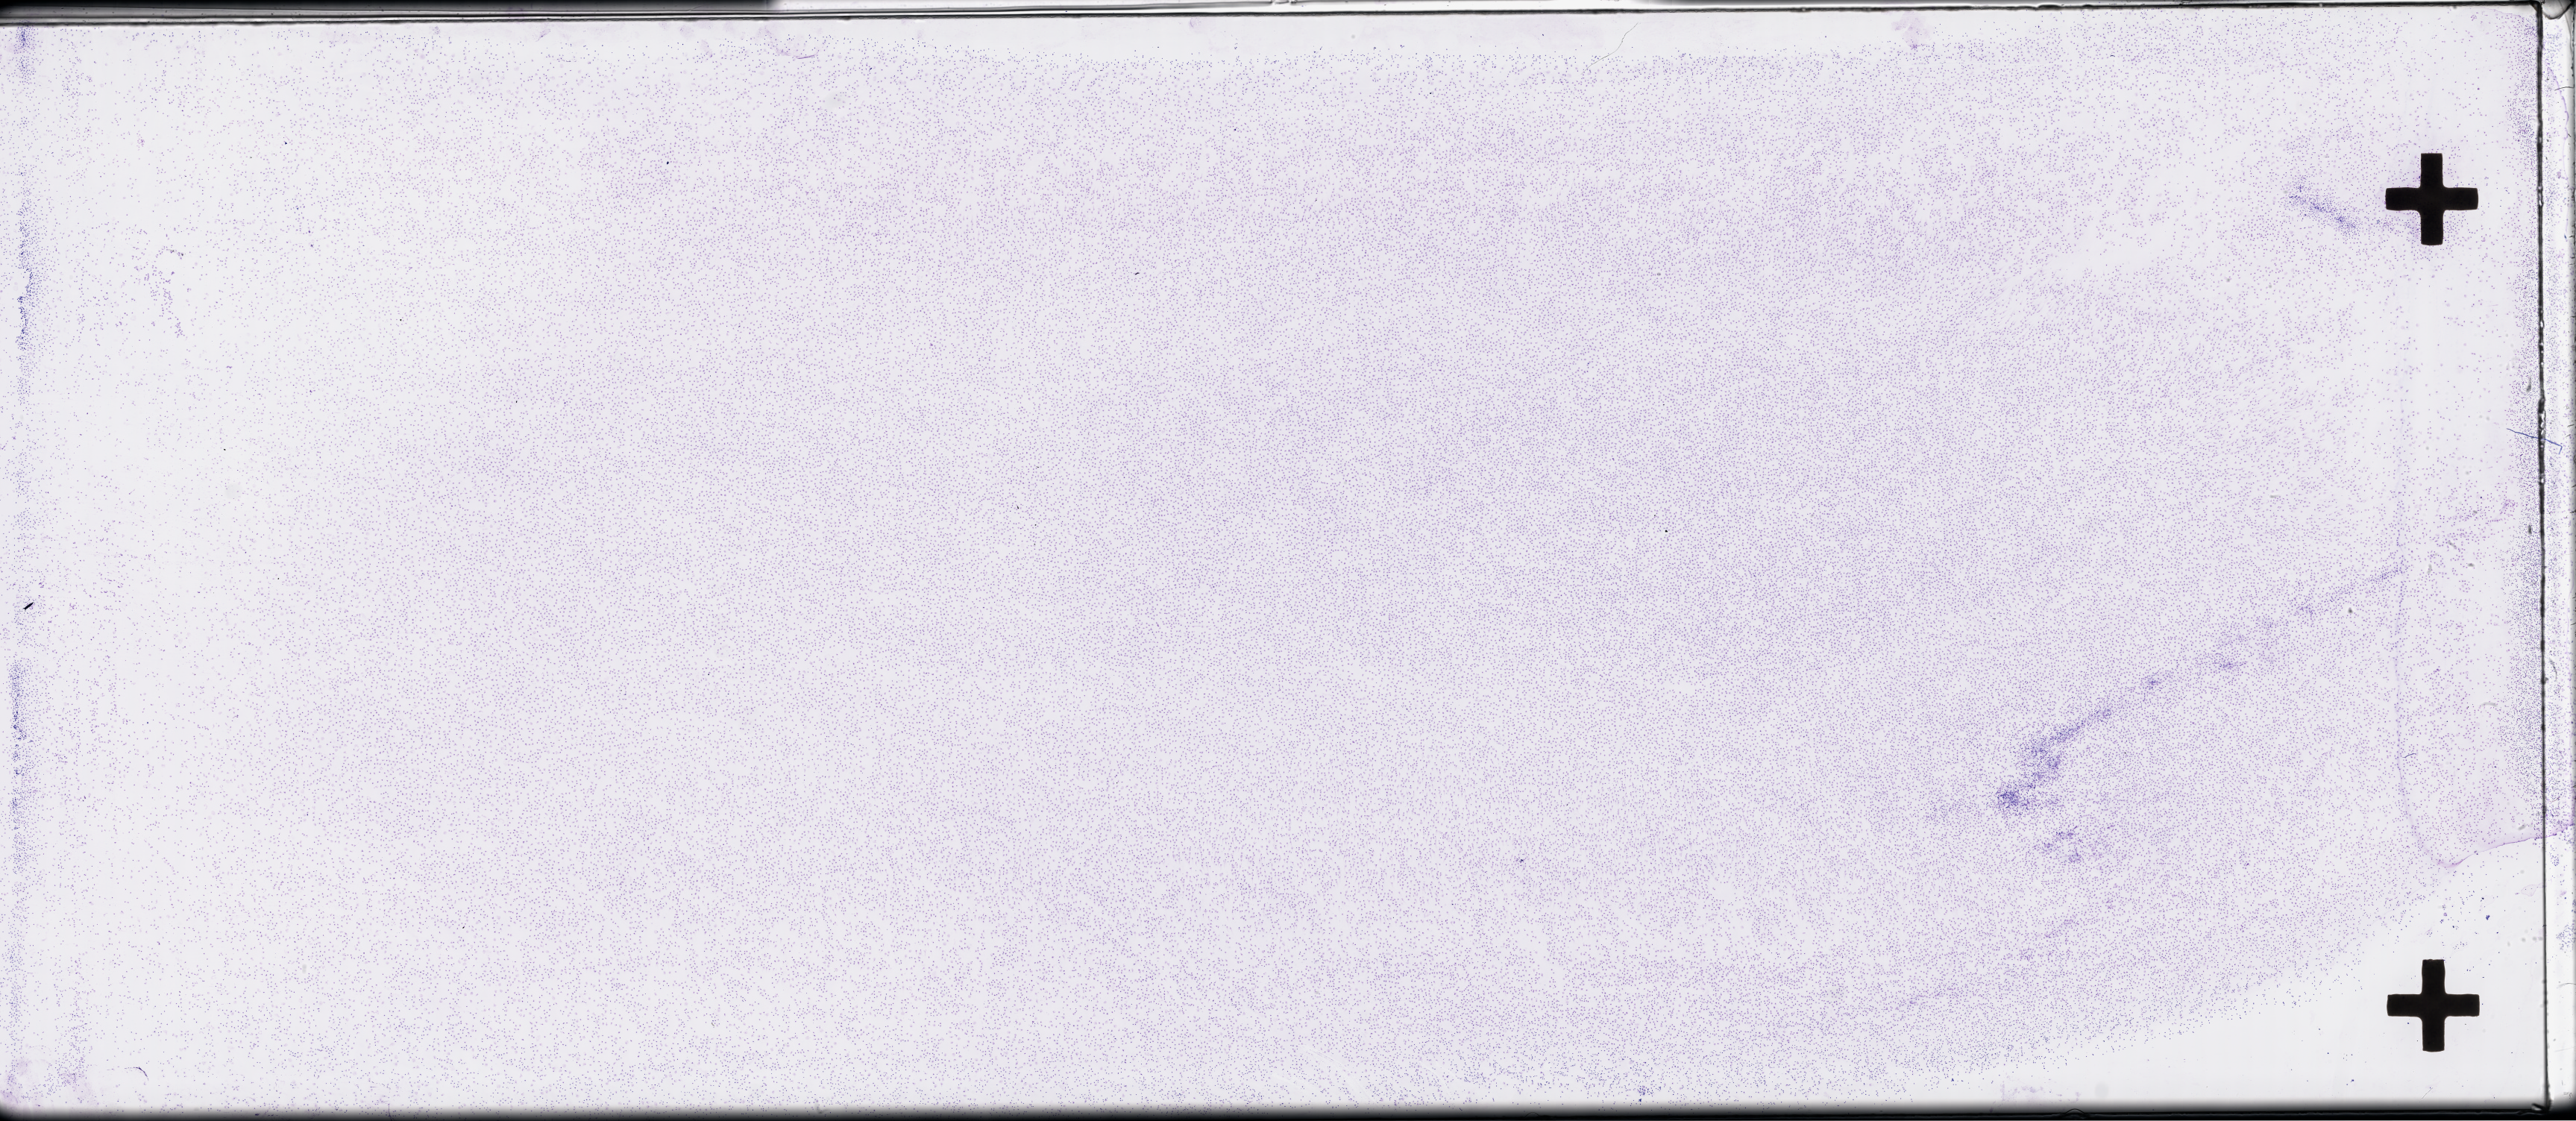
H&E-stained whole-slide image, shown as a low-resolution overview of the whole scanned area (about 55.8 x 24.3 mm, slide scanned at 40x); peripheral blood (leukaemic) sample.
FAB classification: M4. Diagnosis: Acute Myeloid Leukemia.